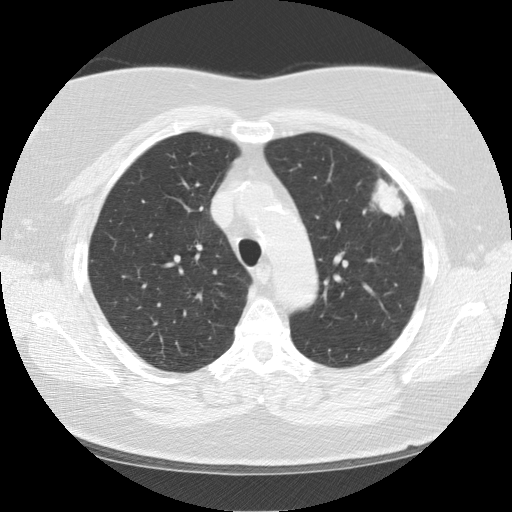
Axial slice from a low-dose chest CT screening exam; baseline annual screen; lung window (W 1500 / L -600 HU); slice 34 of 130 in the series; 512 × 512 image matrix, field of view 350 × 350 mm. Female participant, aged 67 years at enrolment. Former smoker at enrolment.
- Lesion marked by an expert reader, bounding box [x1, y1, x2, y2] px = [349, 161, 421, 228].
- Screening reader's record for this exam (one nodule recorded; not confirmed to be the boxed lesion): non-calcified nodule or mass ≥4 mm, left upper lobe, 28 × 19 mm, soft tissue attenuation.